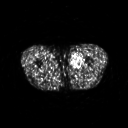
FDG PET of an extremity soft-tissue mass (from a PET/CT study), one axial slice; slice 249 of 311 in the series (ordered by position); 128 × 128 image matrix, field of view 500 × 500 mm. Patient: male, 29 years. From the clinical record (not read from this slice): histological type: mixoid liposarcoma; grade: low; site of the primary tumour: left thigh.
Annotated regions visible in this slice (expert contour drawn on MRI and transferred to this co-registered scan by the dataset authors):
- gross tumour volume (mass): bounding box [x1, y1, x2, y2] px = [70, 53, 83, 68]